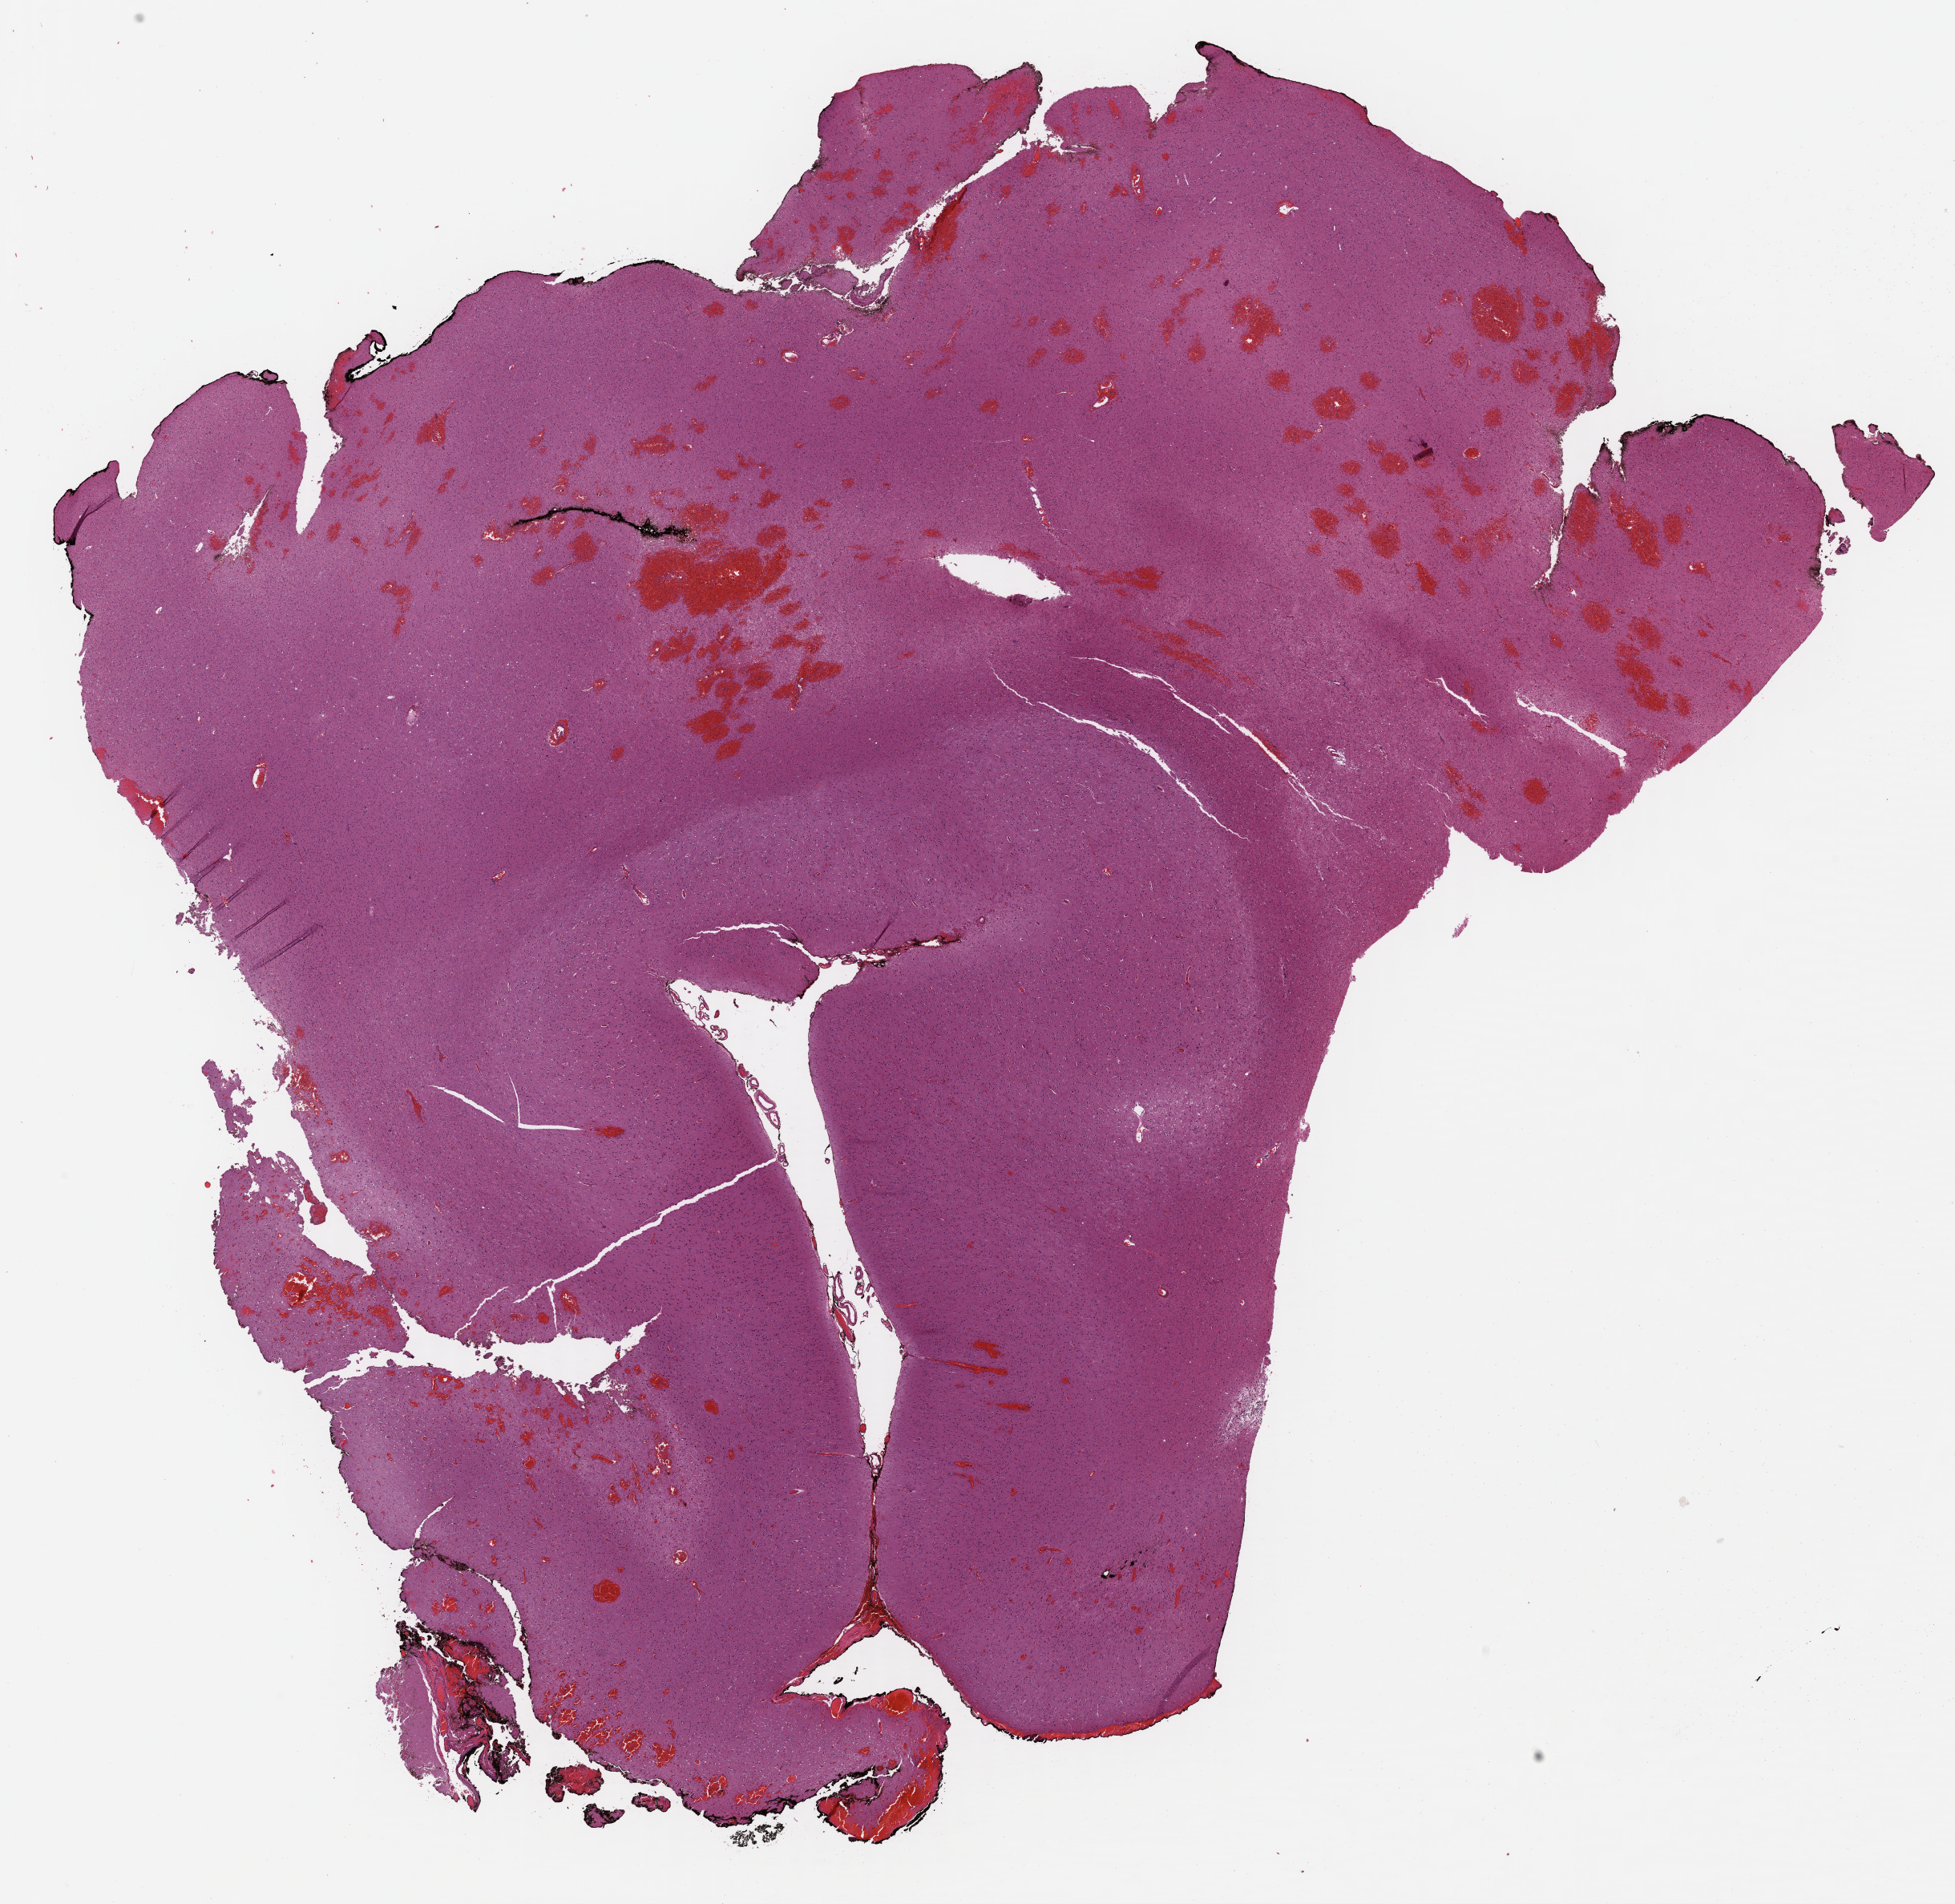
H&E-stained whole-slide image — a low-resolution overview of the entire scanned area, about 19.2 x 18.7 mm; formalin-fixed paraffin-embedded (FFPE) diagnostic section; sample: primary tumour, brain. Female patient; age at initial diagnosis 61 years. Histologic grade: G2 (moderately differentiated).
Histologic diagnosis: Astrocytoma, NOS (cerebrum). Laterality: left.